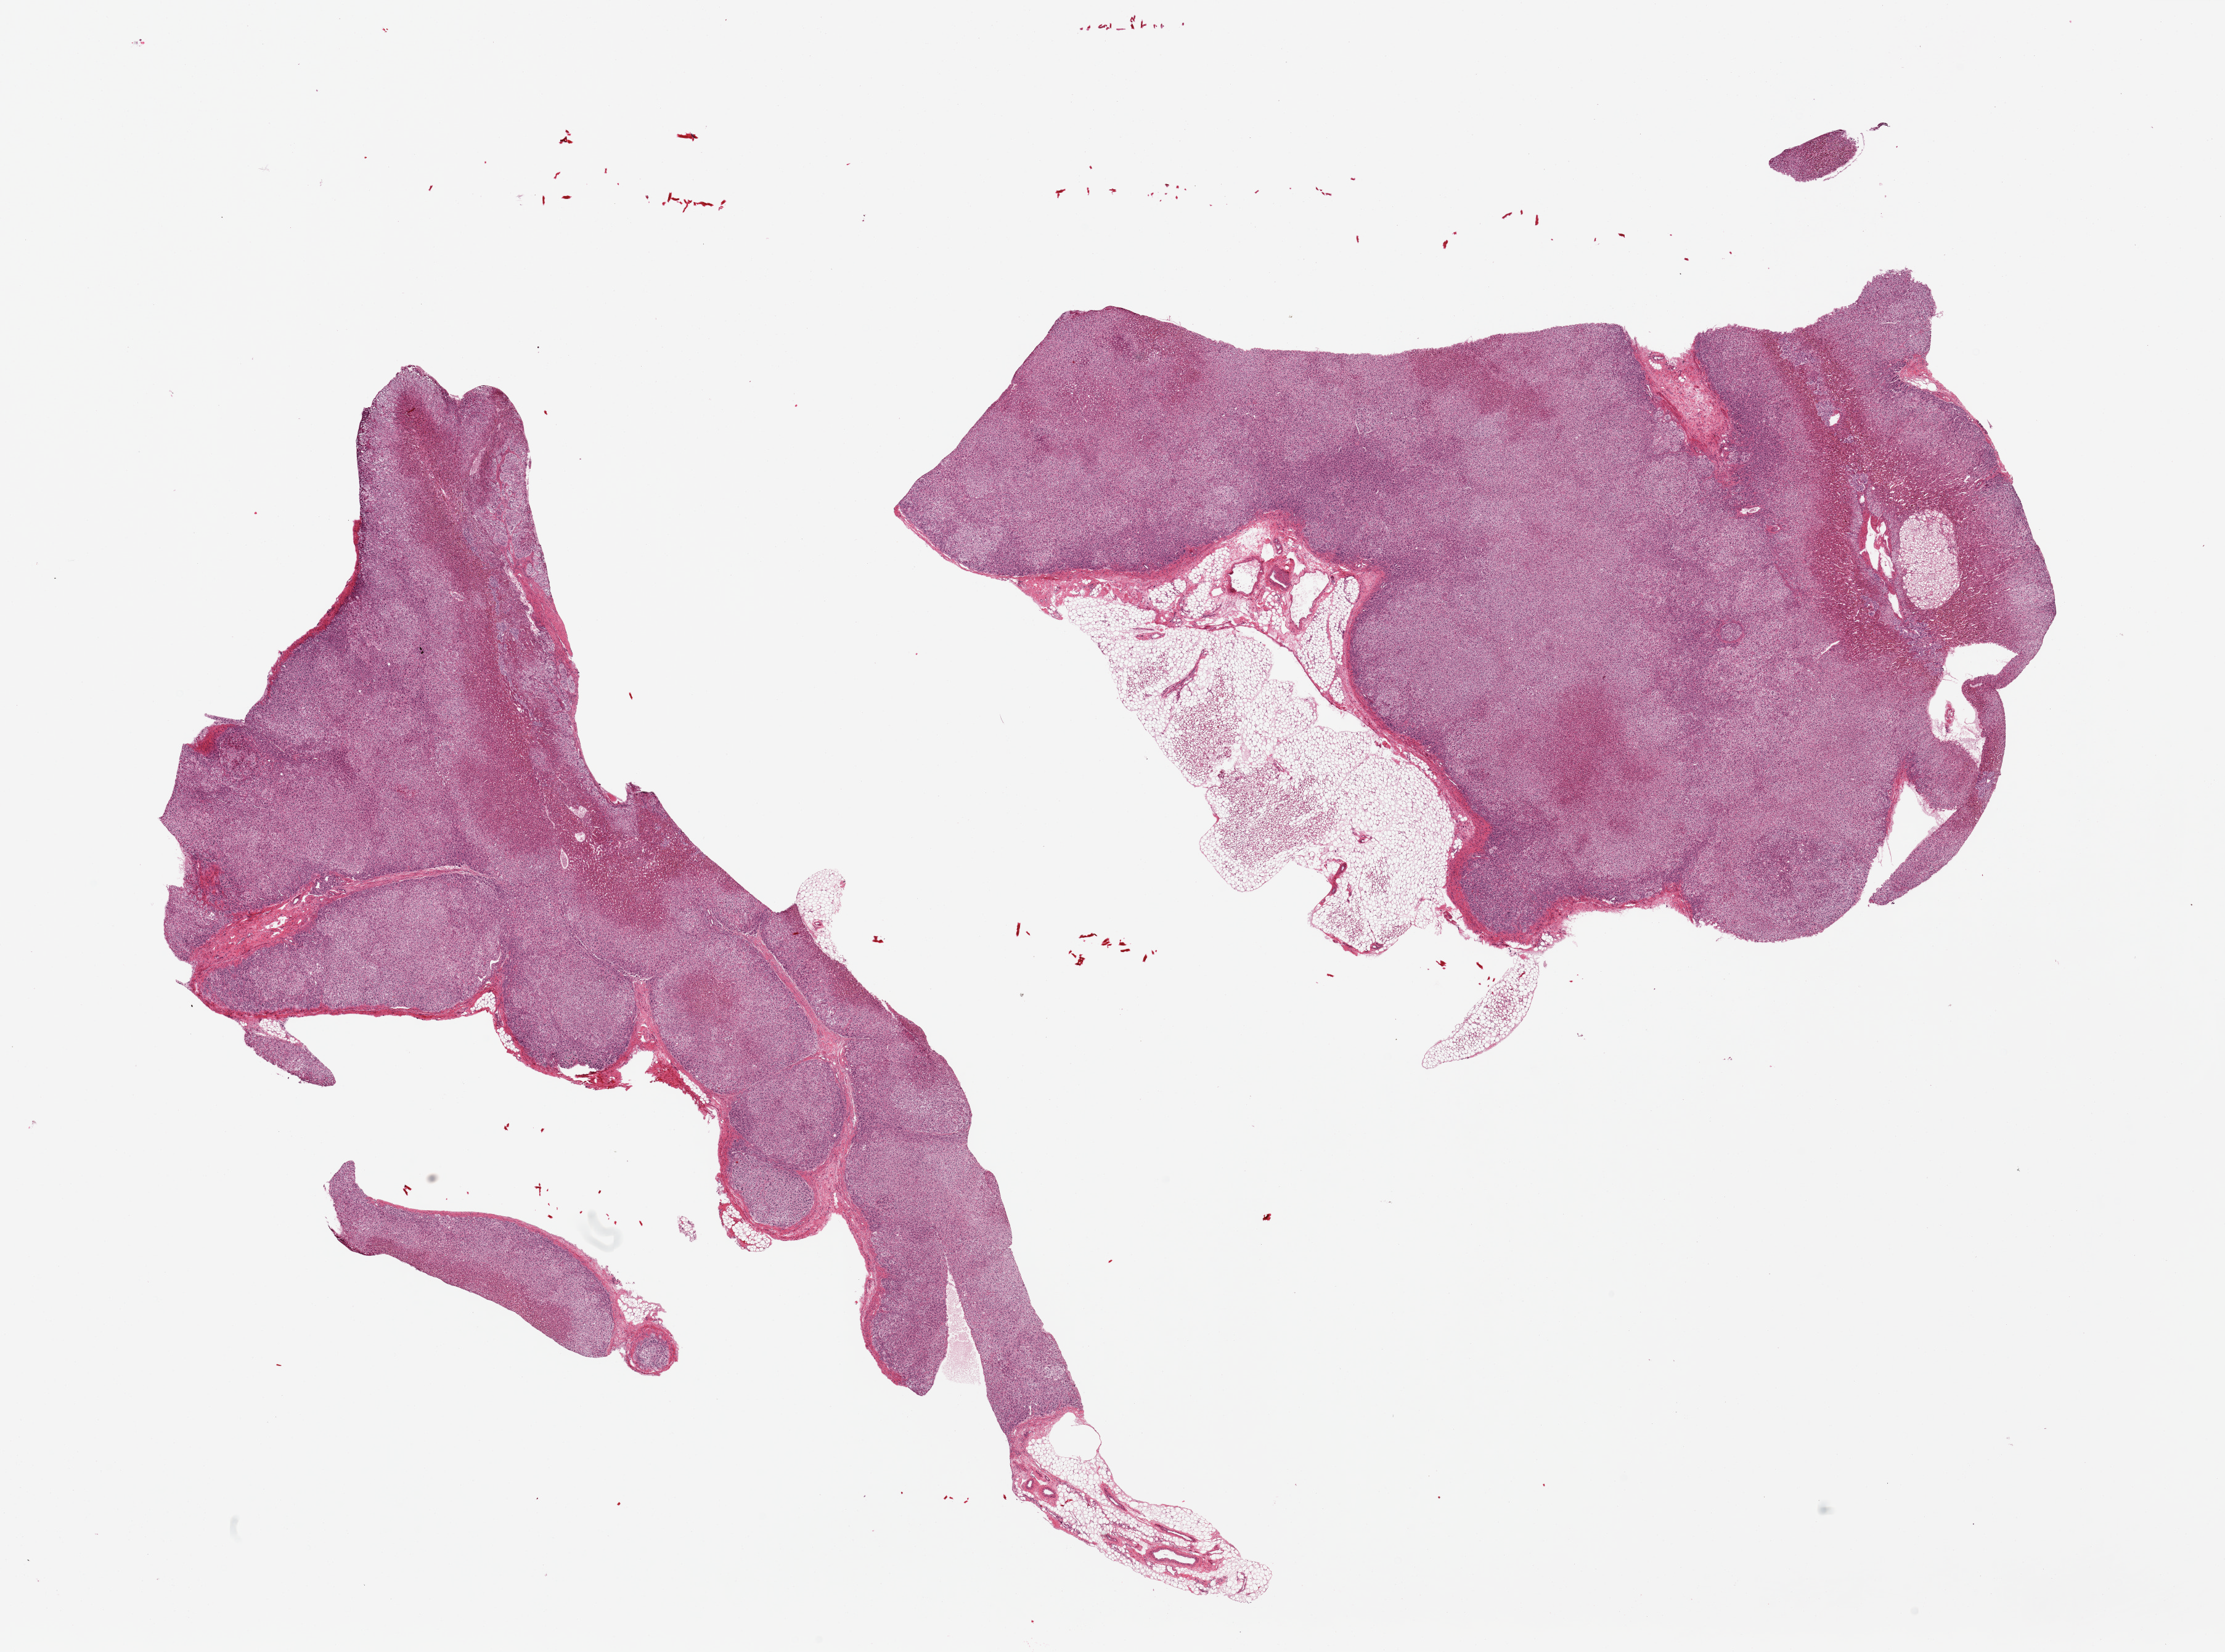
Digitized hematoxylin and eosin (H&E)-stained section, a low-resolution overview of the entire scanned area, about 28.5 x 21.2 mm (acquisition: 20x scan), PAXgene-fixed, paraffin-embedded tissue, sampled site (target tissue): adrenal gland, tissue donor sample. Female donor.
Reviewer comment on this tissue sample: 2 pieces, all cortex.